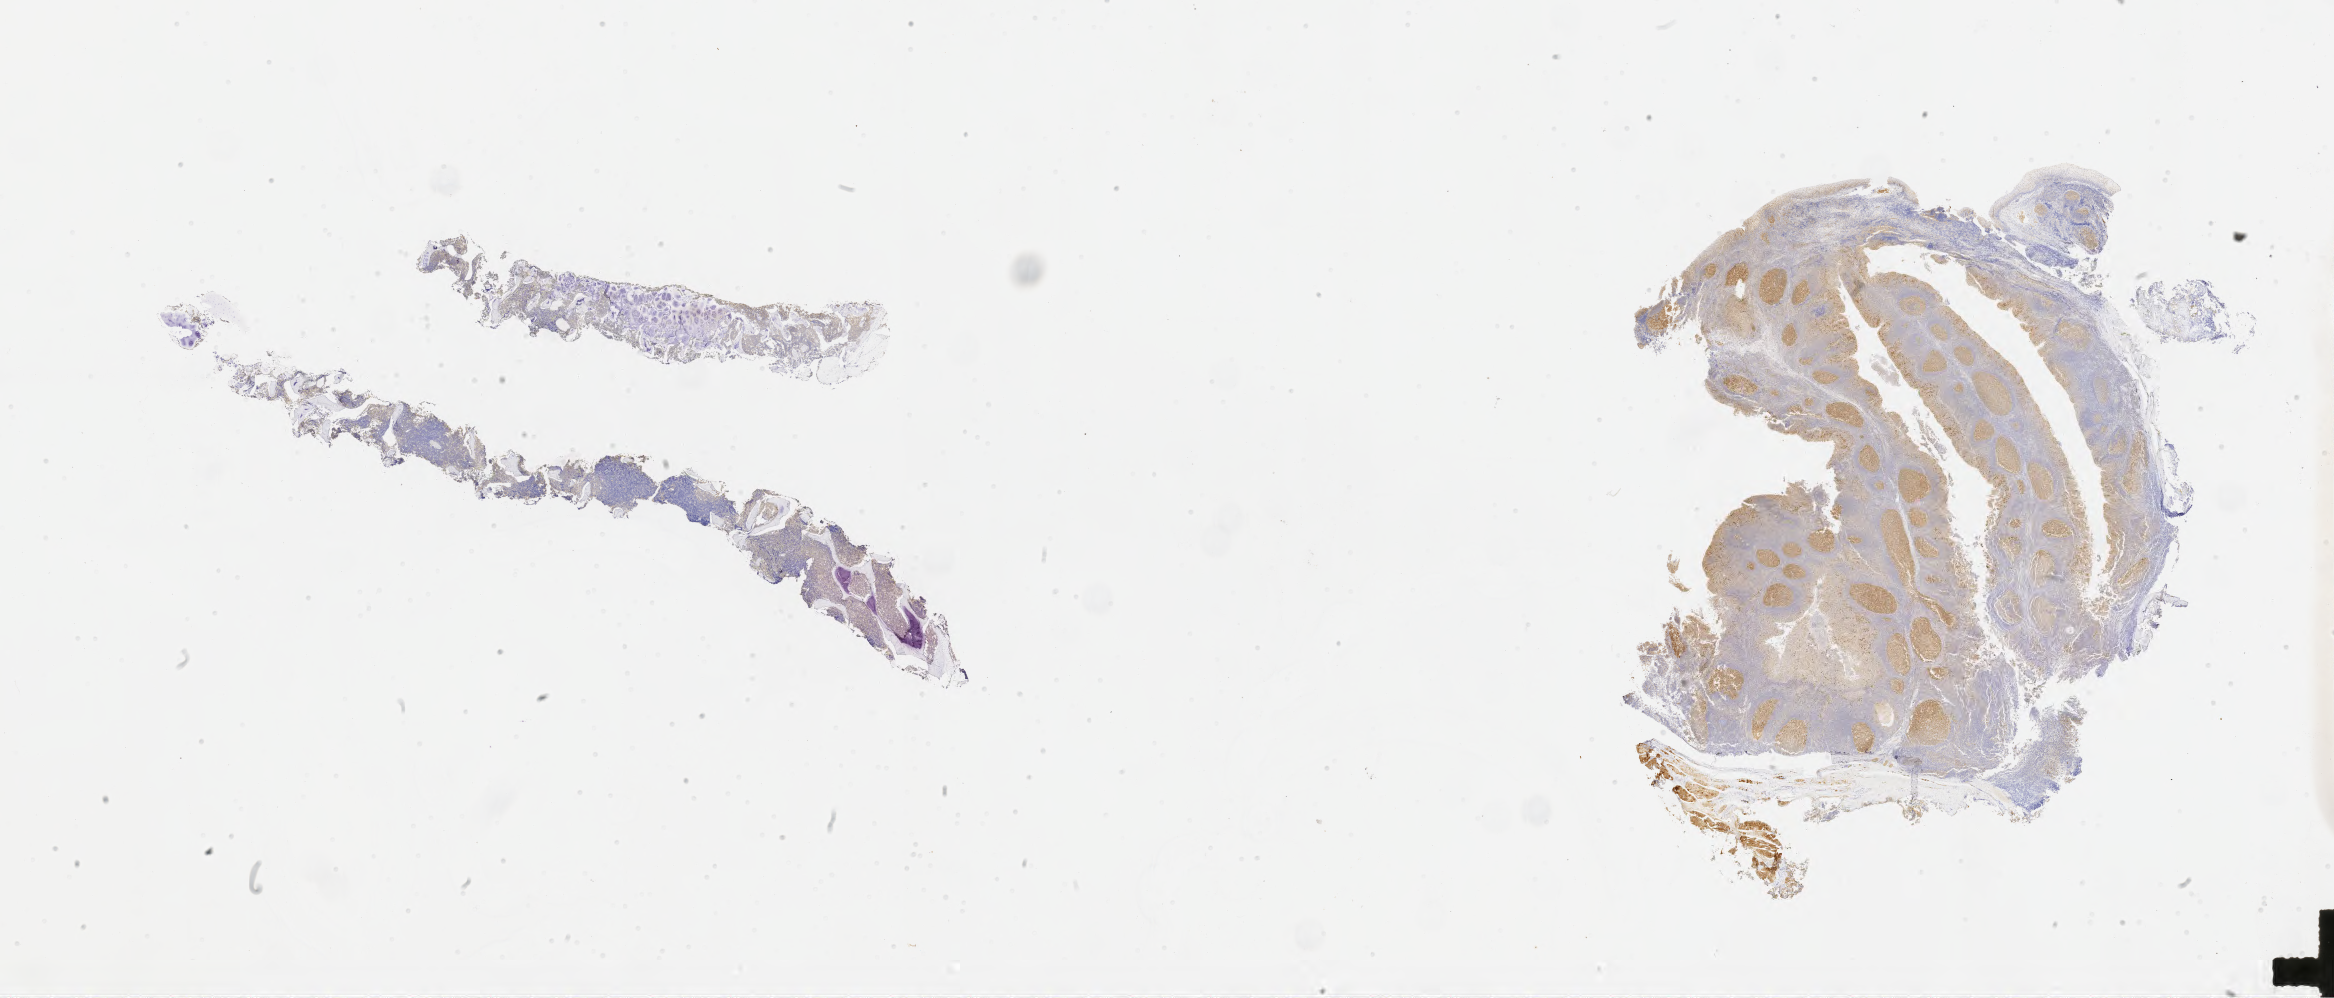
Whole-slide image, immunohistochemical stain for BCL6, whole scanned area (about 37.7 x 16.1 mm) shown as a low-resolution overview, specimen: tumor tissue, anatomic site: bone marrow. Patient male; aged 11.
Diagnosis: Burkitt lymphoma, NOS.